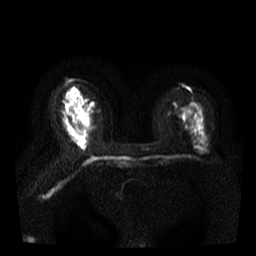
Breast MRI, one axial slice; diffusion-weighted series; image 2 of 4 stored at this slice position (different b-values; order by instance number); 3 T; 5 mm slice thickness; 256 × 256 image matrix, field of view 300 × 300 mm. Female patient.
Annotated regions visible in this slice (expert manual segmentation):
- tumour on diffusion-weighted imaging: bounding box (x1, y1, x2, y2) in pixels: (73, 104, 87, 123)